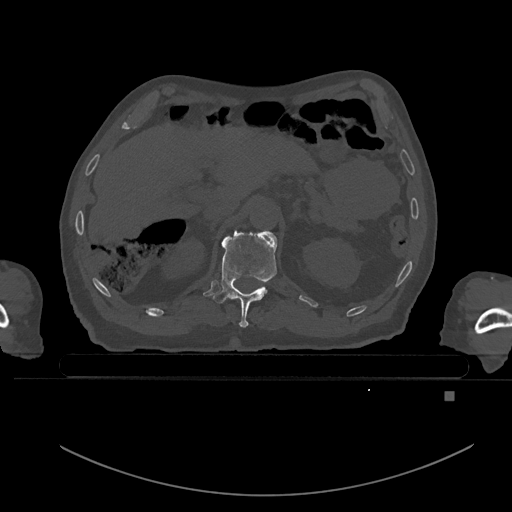
CT including the spine, one axial slice; position 21 of 969 along the scan axis; bone window (W 1800 / L 400 HU); 512 × 512 image matrix, field of view 456 × 456 mm. Male patient, age 82 years. From the clinical record (not read from this slice): primary cancer: prostate; vertebrae with lytic lesions (as recorded): T11, T9, T8, T2.
Outlined on this slice (semi-automatic segmentation, software-assisted and operator-edited):
- T11 vertebra: bounding box (x1, y1, x2, y2) in pixels: (213, 231, 277, 328)